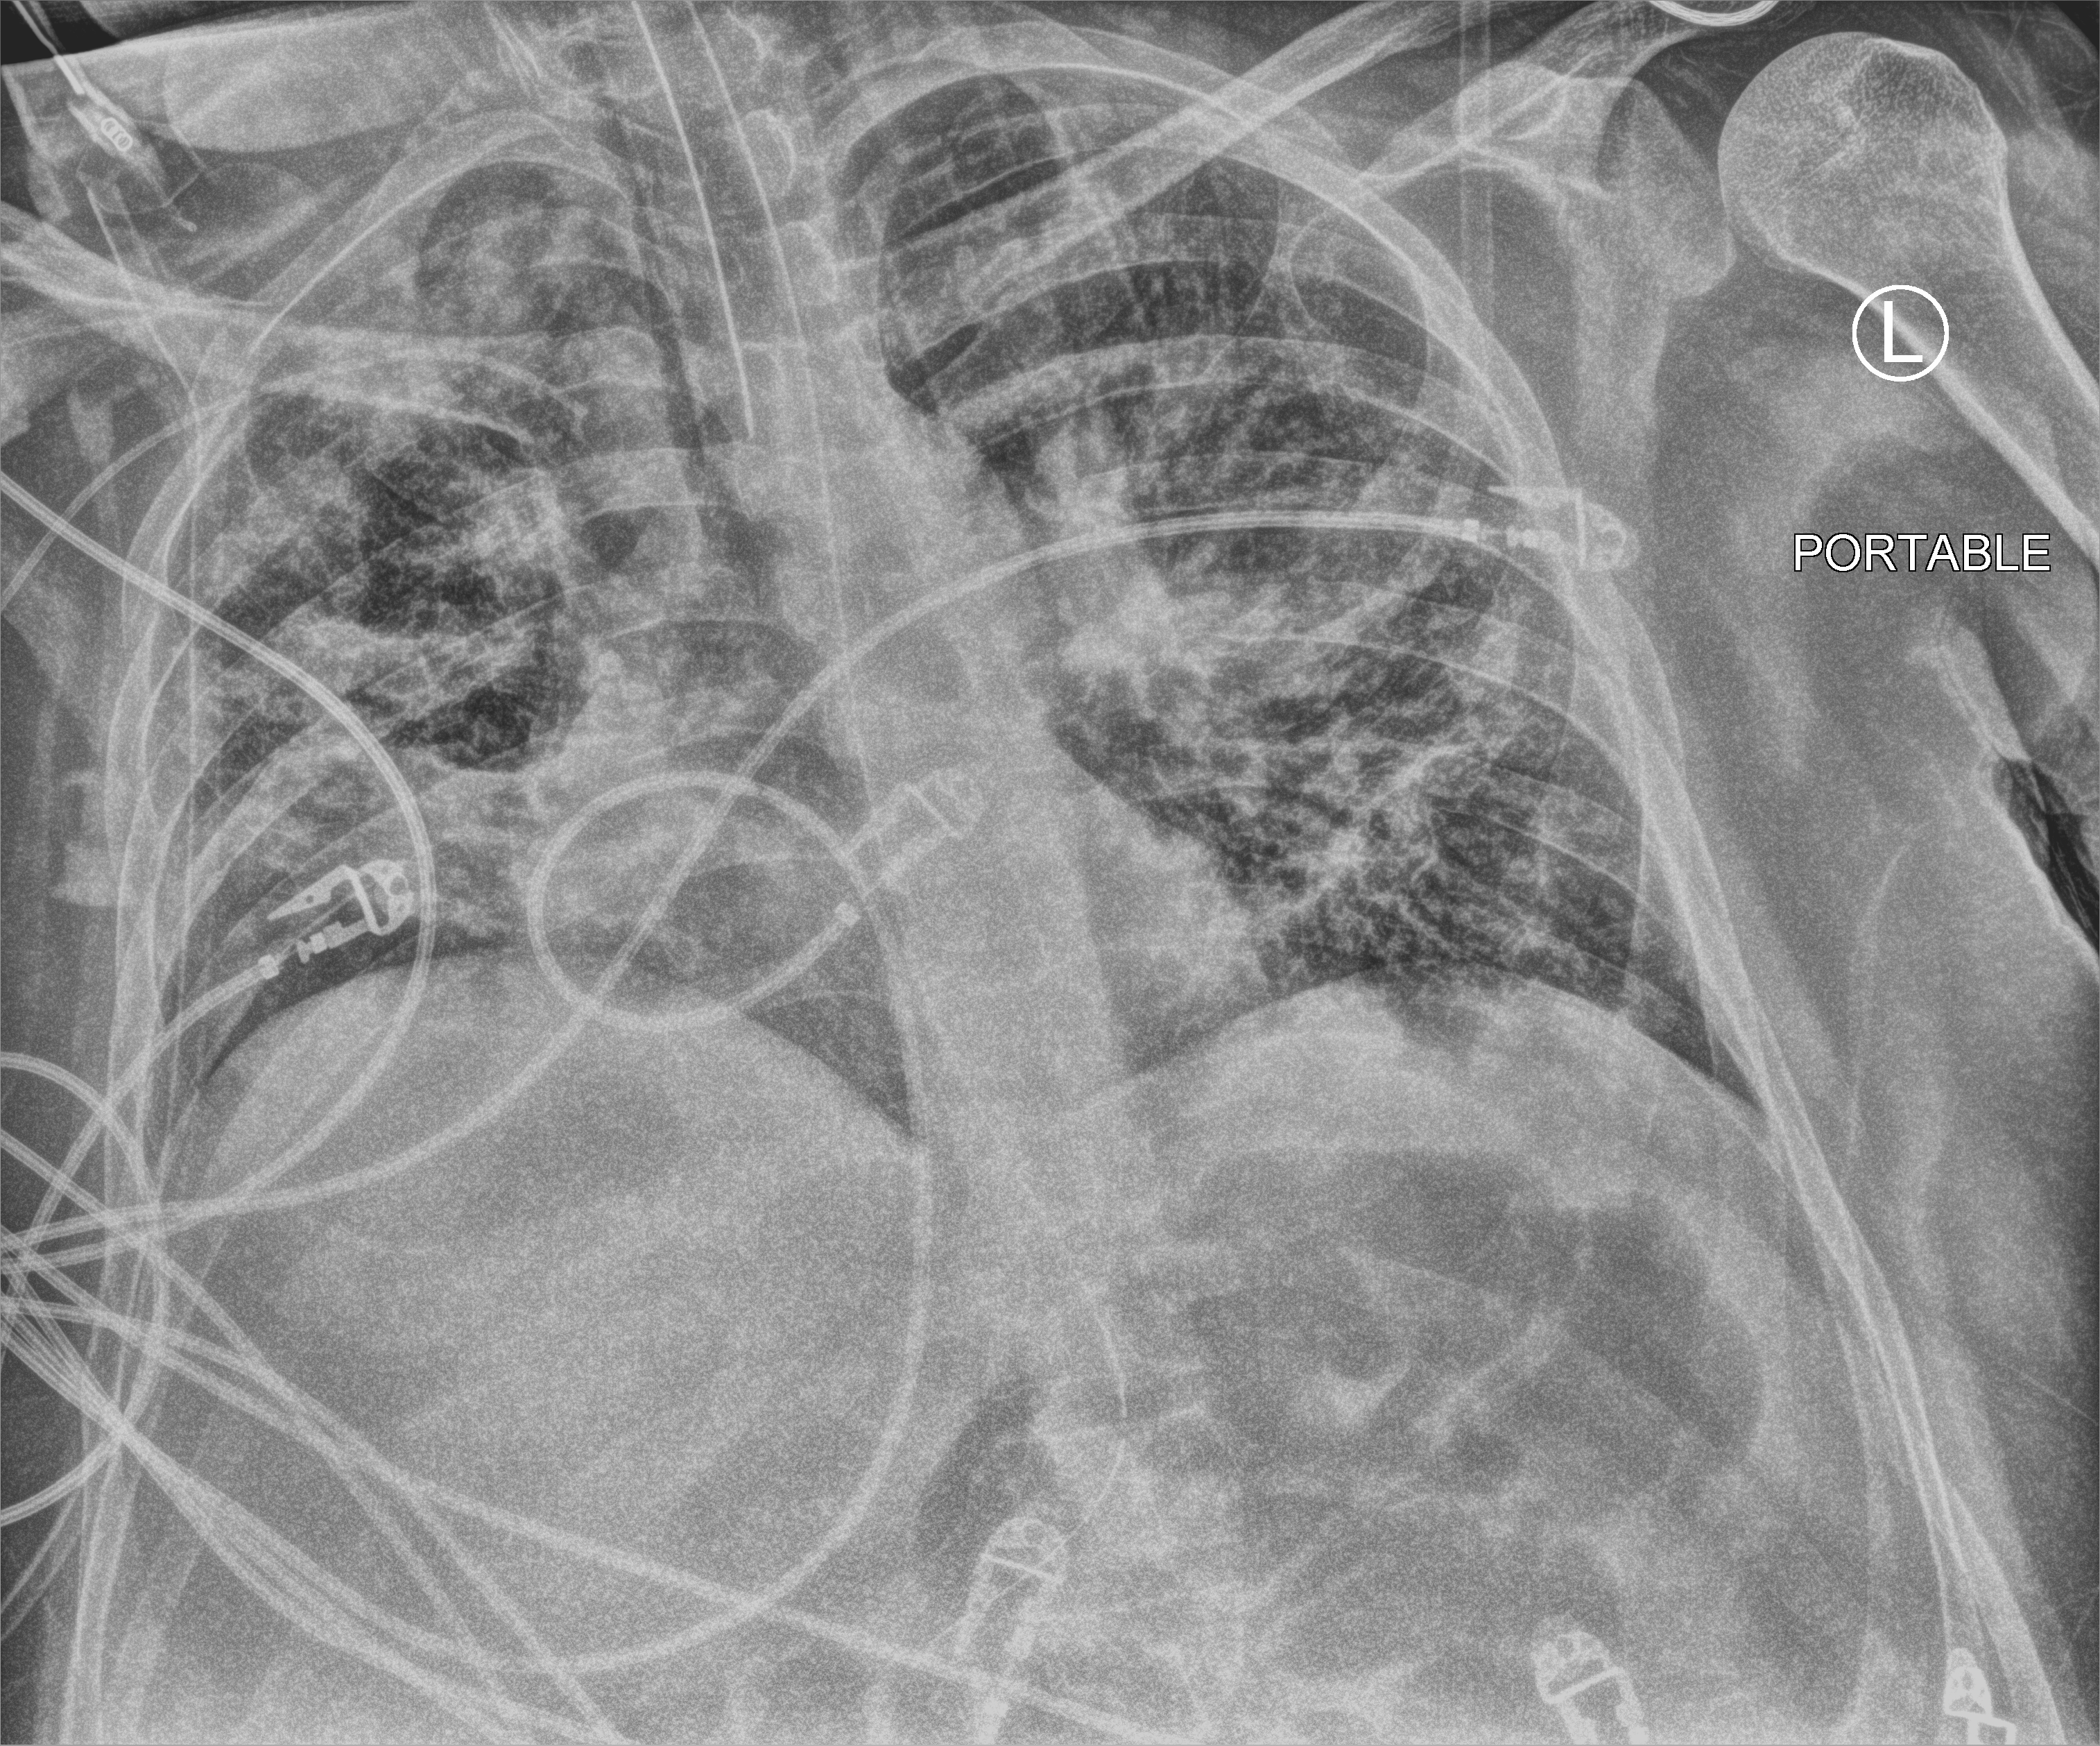
Chest X-ray (portable). Patient hospitalised with COVID-19, aged 18–59 years.
Hospital-stay facts (about this admission, not read from this image; timing relative to this image not recorded): admitted to intensive care during this hospital stay: yes; smoking status (admission record): never; diabetes (admission record): no.